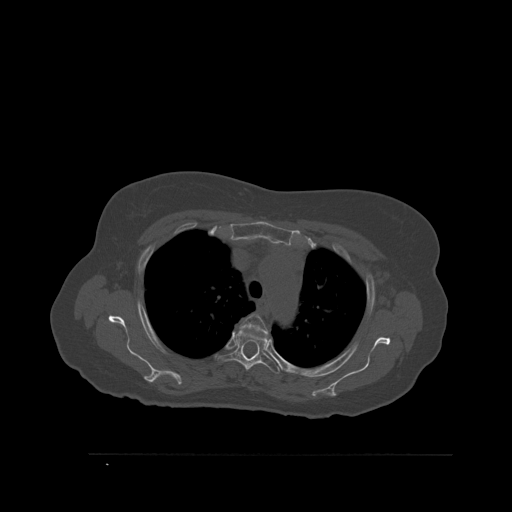
CT including the spine, one axial slice. Position 411 of 527 along the scan axis. Bone window (W 1800 / L 400 HU). 512 × 512 image matrix, field of view 470 × 470 mm. Patient: female, 73 years. Case-level facts recorded for this patient, not image findings: primary cancer: breast; vertebrae with lytic lesions (as recorded): L2.
Outlined on this slice (semi-automatically segmented with operator editing):
- T3 vertebra: bounding box <240,314,269,339> (left, top, right, bottom; pixels)
- T4 vertebra: <221,330,280,374>